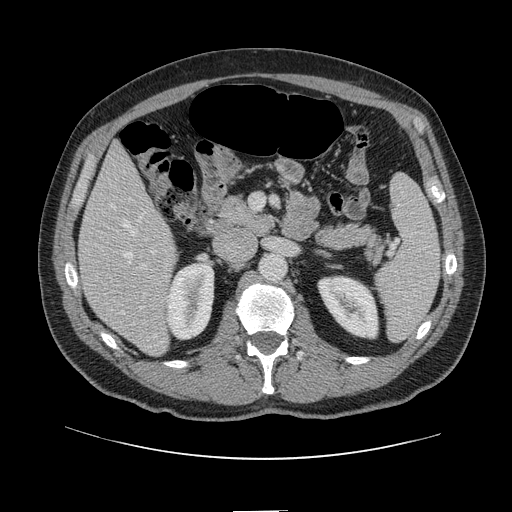
Contrast-enhanced abdominal CT, one axial slice. Slice 54 of 161 in the series (ordered by position). Intravenous contrast given. Soft-tissue window (W 400 / L 40 HU). 2.5 mm slice thickness. 512 × 512 image matrix, field of view 412 × 412 mm. Male patient, age 66 years. From the clinical record (not read from this slice): diagnosis: colorectal cancer liver metastases, imaged before liver resection.
Structures marked on this image (expert manual segmentation):
- hepatic veins: bounding box [x1, y1, x2, y2] px = [114, 207, 135, 258]
- liver: [79, 144, 177, 356]
- planned liver remnant (the part of the liver to remain after resection): [79, 145, 165, 279]
- portal vein (with intrahepatic branches): [127, 248, 157, 297]